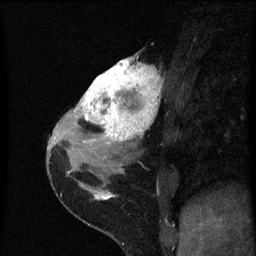
Breast MRI (dynamic contrast-enhanced), one sagittal slice; position 28 of 60 along the scan axis; dynamic contrast-enhanced series, image 2 of 3 at this slice position (ordered by acquisition); 1.5 T; TE 4.2 ms, TR 8 ms; 2 mm slice thickness; 256 × 256 image matrix, field of view 180 × 180 mm. Female patient, age 38 years.
Outlined on this slice (semi-automatic segmentation, software-assisted and operator-edited):
- analysis volume of interest (the breast-tissue region the enhancement analysis was run in; not a lesion): bounding box <80,56,161,151> (left, top, right, bottom; pixels)
- tumour enhancement mask (voxels above the 70 % enhancement threshold inside the analysis volume of interest): <80,58,161,149>